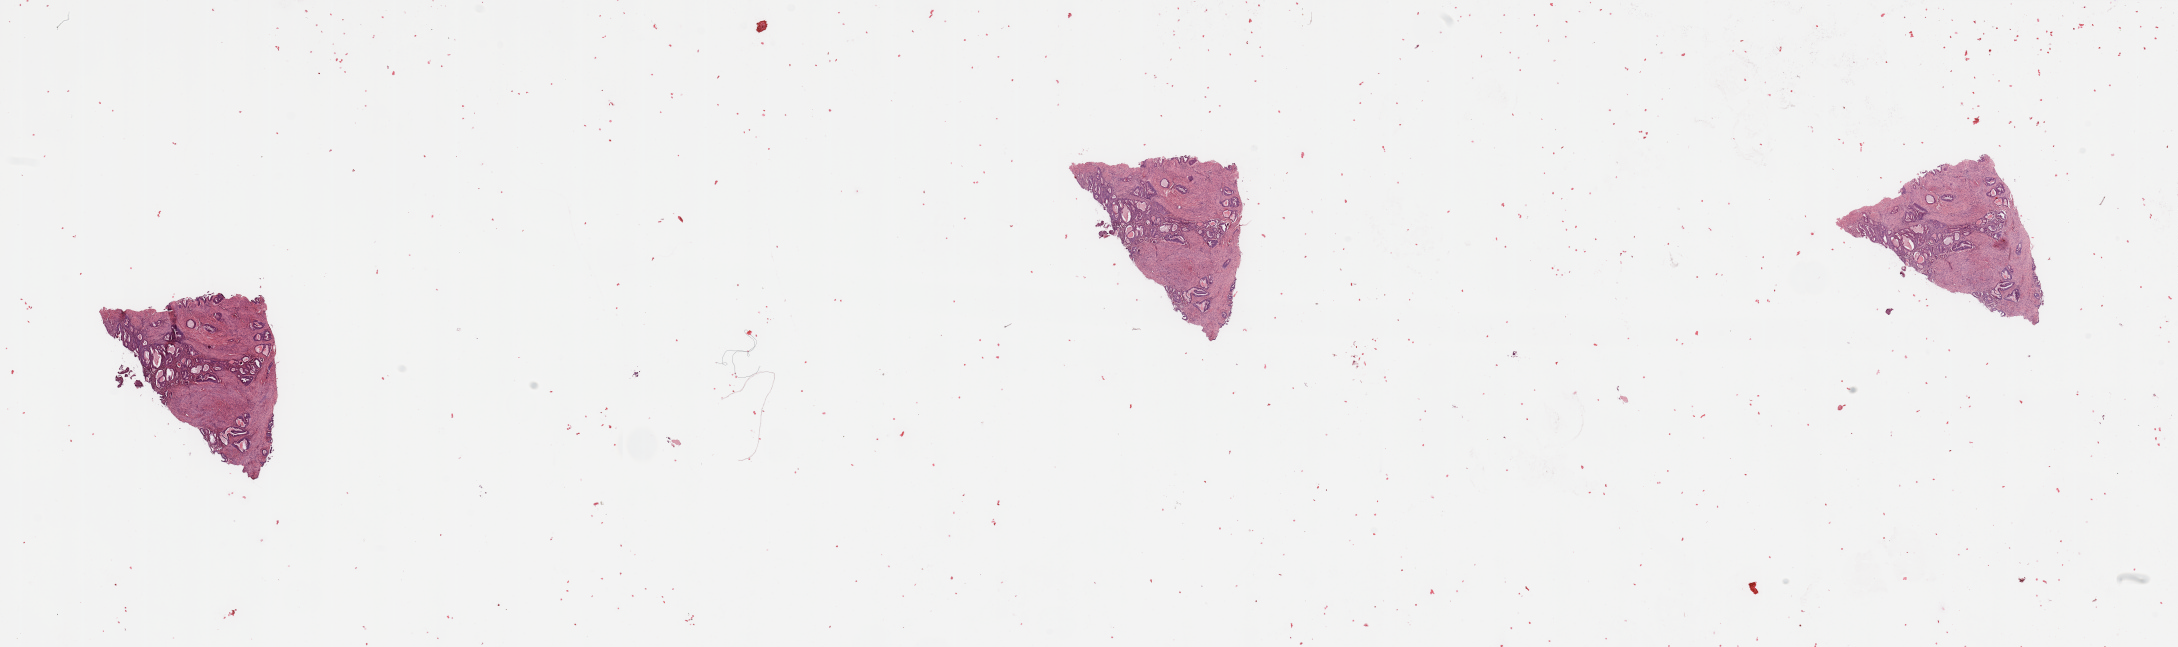
Digitized Hematoxylin and eosin (H&E) stained tissue section (whole slide) — a low-resolution overview of the entire scanned area, about 34.5 x 10.2 mm. Uterus, normal (non-tumour) tissue. Patient: female, age 69 years.
• this section: normal (non-tumour) tissue from the same patient
• patient diagnosis (cohort enrolment): corpus endometrial carcinoma (uterus)